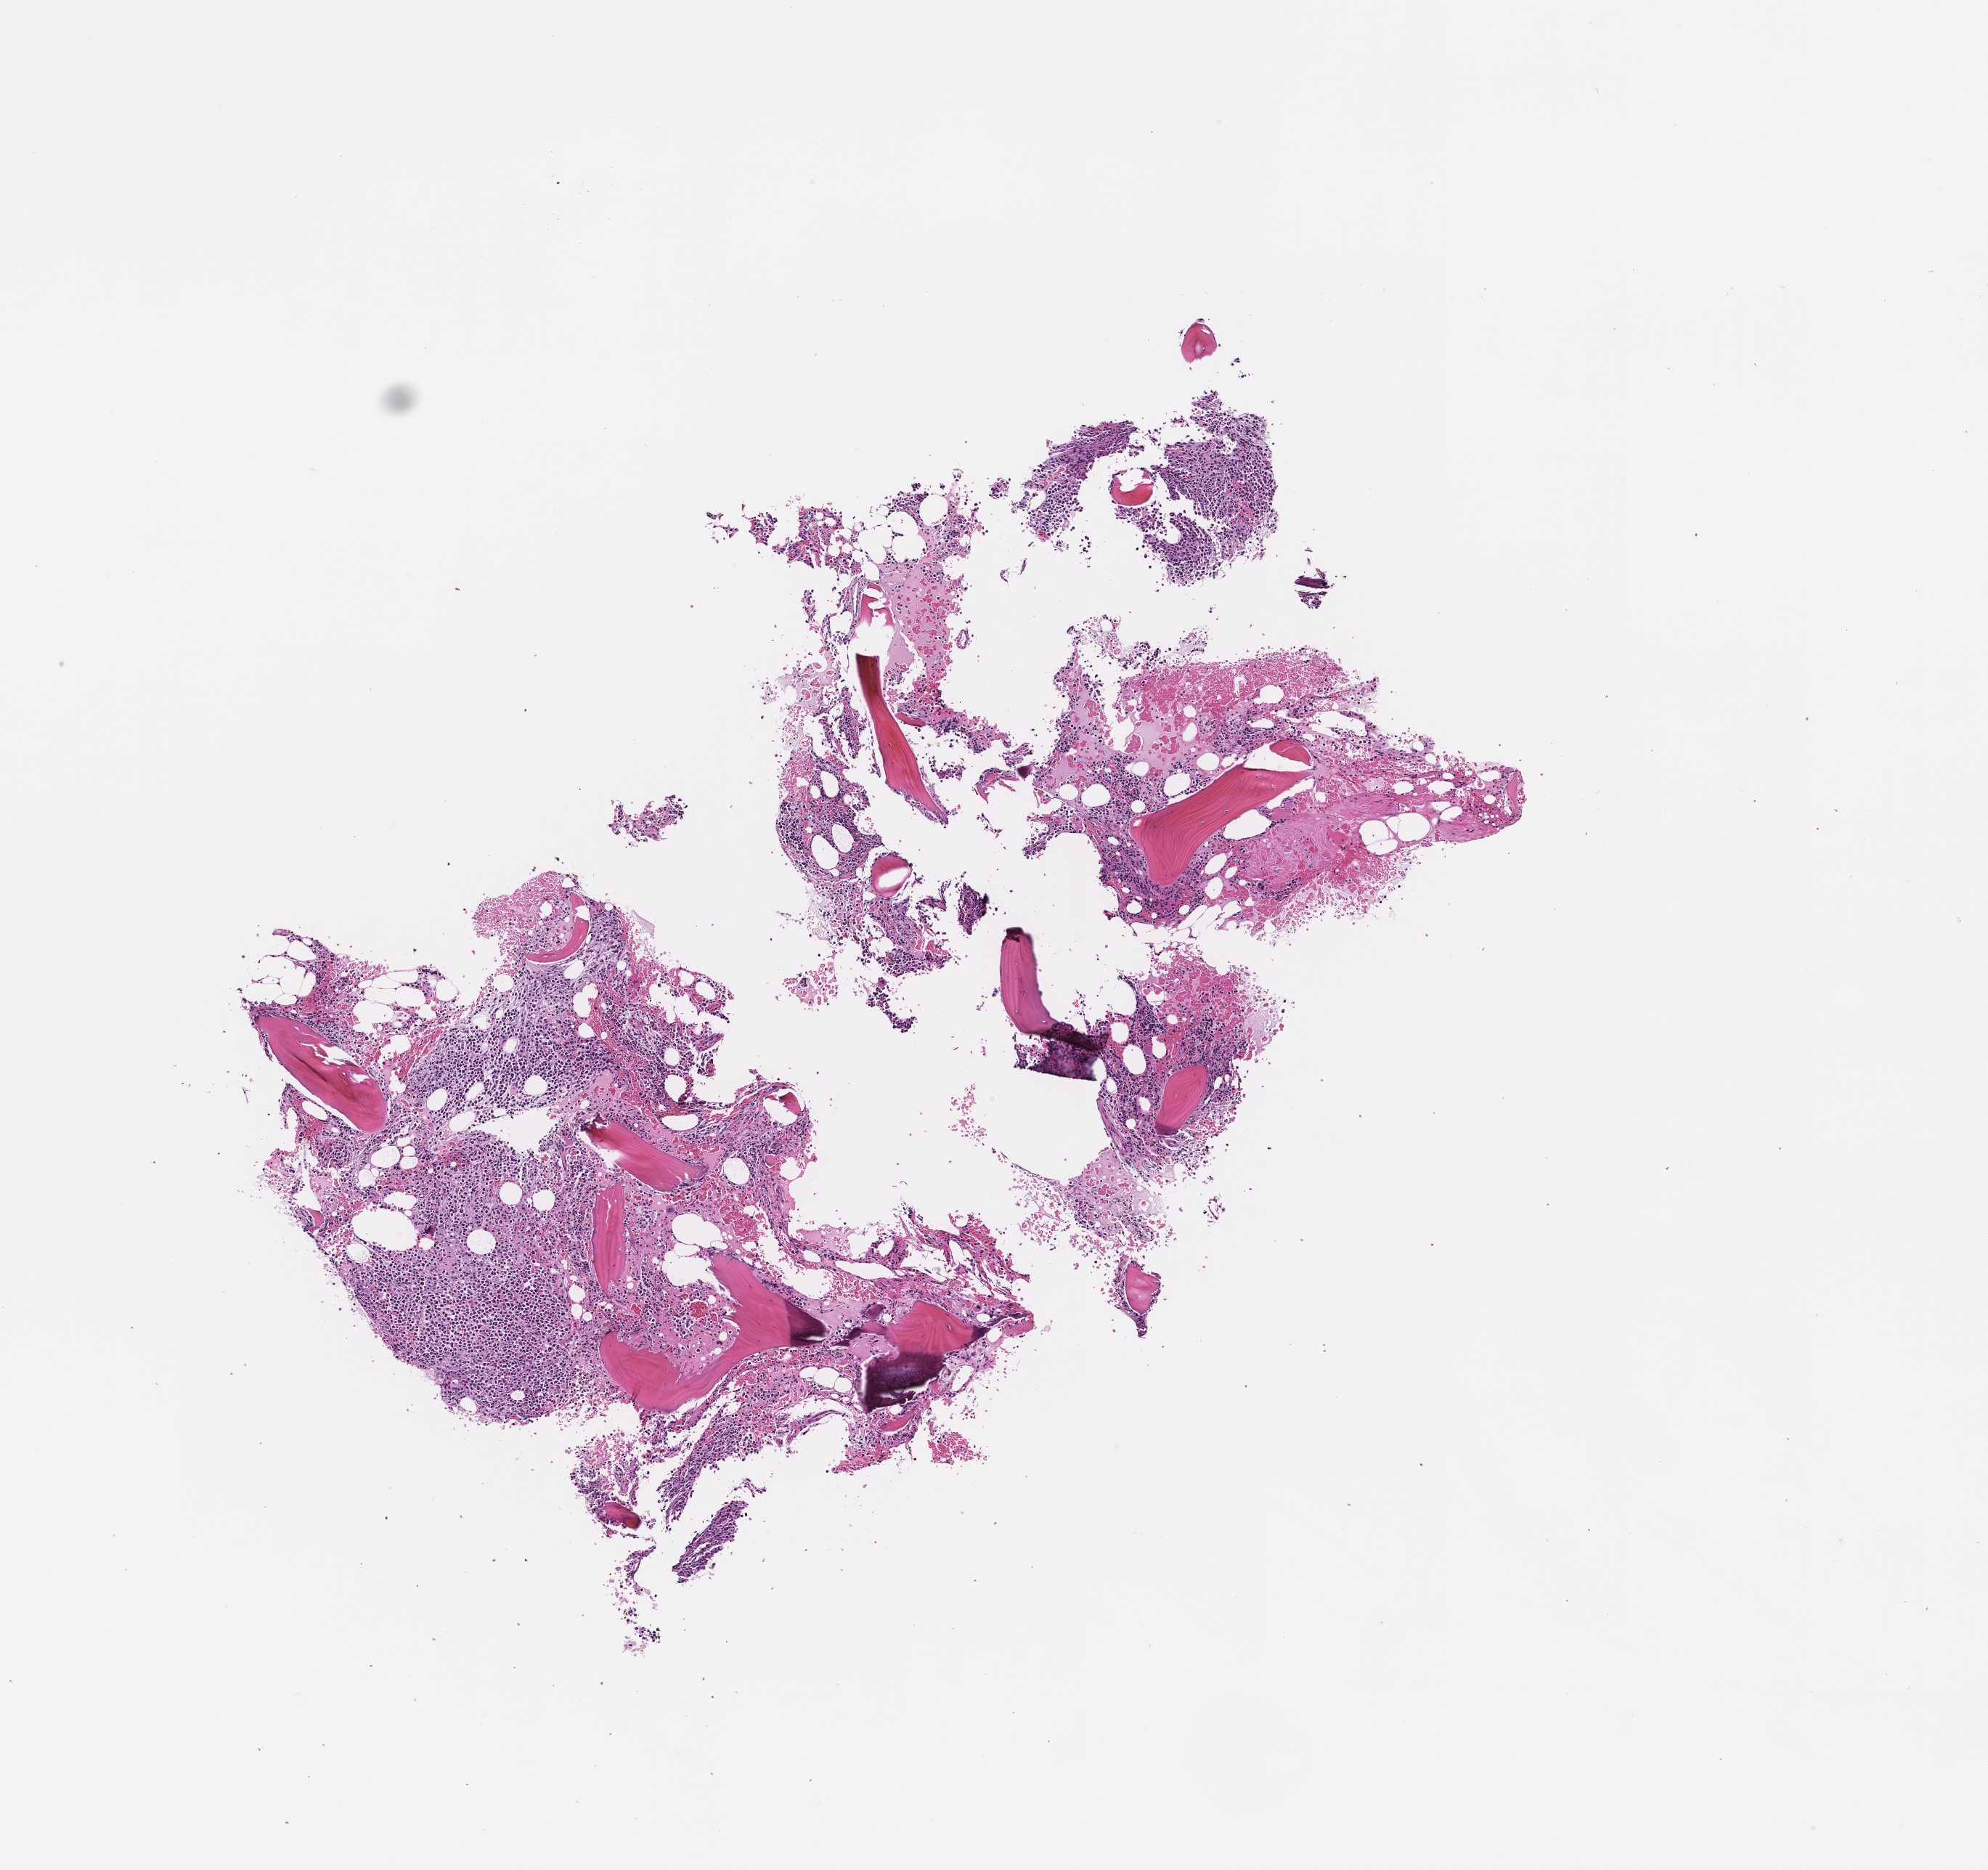
Haematoxylin and eosin whole-slide image, a low-resolution overview of the entire scanned area, about 5.5 x 5.2 mm; formalin-fixed, paraffin-embedded (FFPE) tissue; site: bone marrow; specimen time point: collected at baseline (before treatment). Patient sex: male.
• this section: primary tumour tissue
• diagnosis: Plasma Cell Myeloma